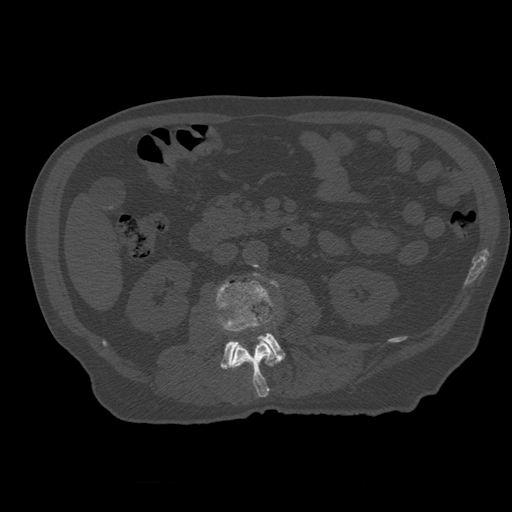
CT including the spine, one axial slice. Position 201 of 399 along the scan axis. 120 kVp. Bone window (W 1800 / L 400 HU). 1.25 mm slice thickness. 512 × 512 image matrix, field of view 407 × 407 mm. Patient age 73 years. From the clinical record (not read from this slice): primary cancer: prostate; vertebrae with lytic lesions (as recorded): L2.
Structures marked on this image (semi-automatic segmentation, software-assisted and operator-edited):
- L2 vertebra: bounding box [x1, y1, x2, y2] px = [230, 320, 276, 398]
- L3 vertebra: [217, 273, 285, 370]